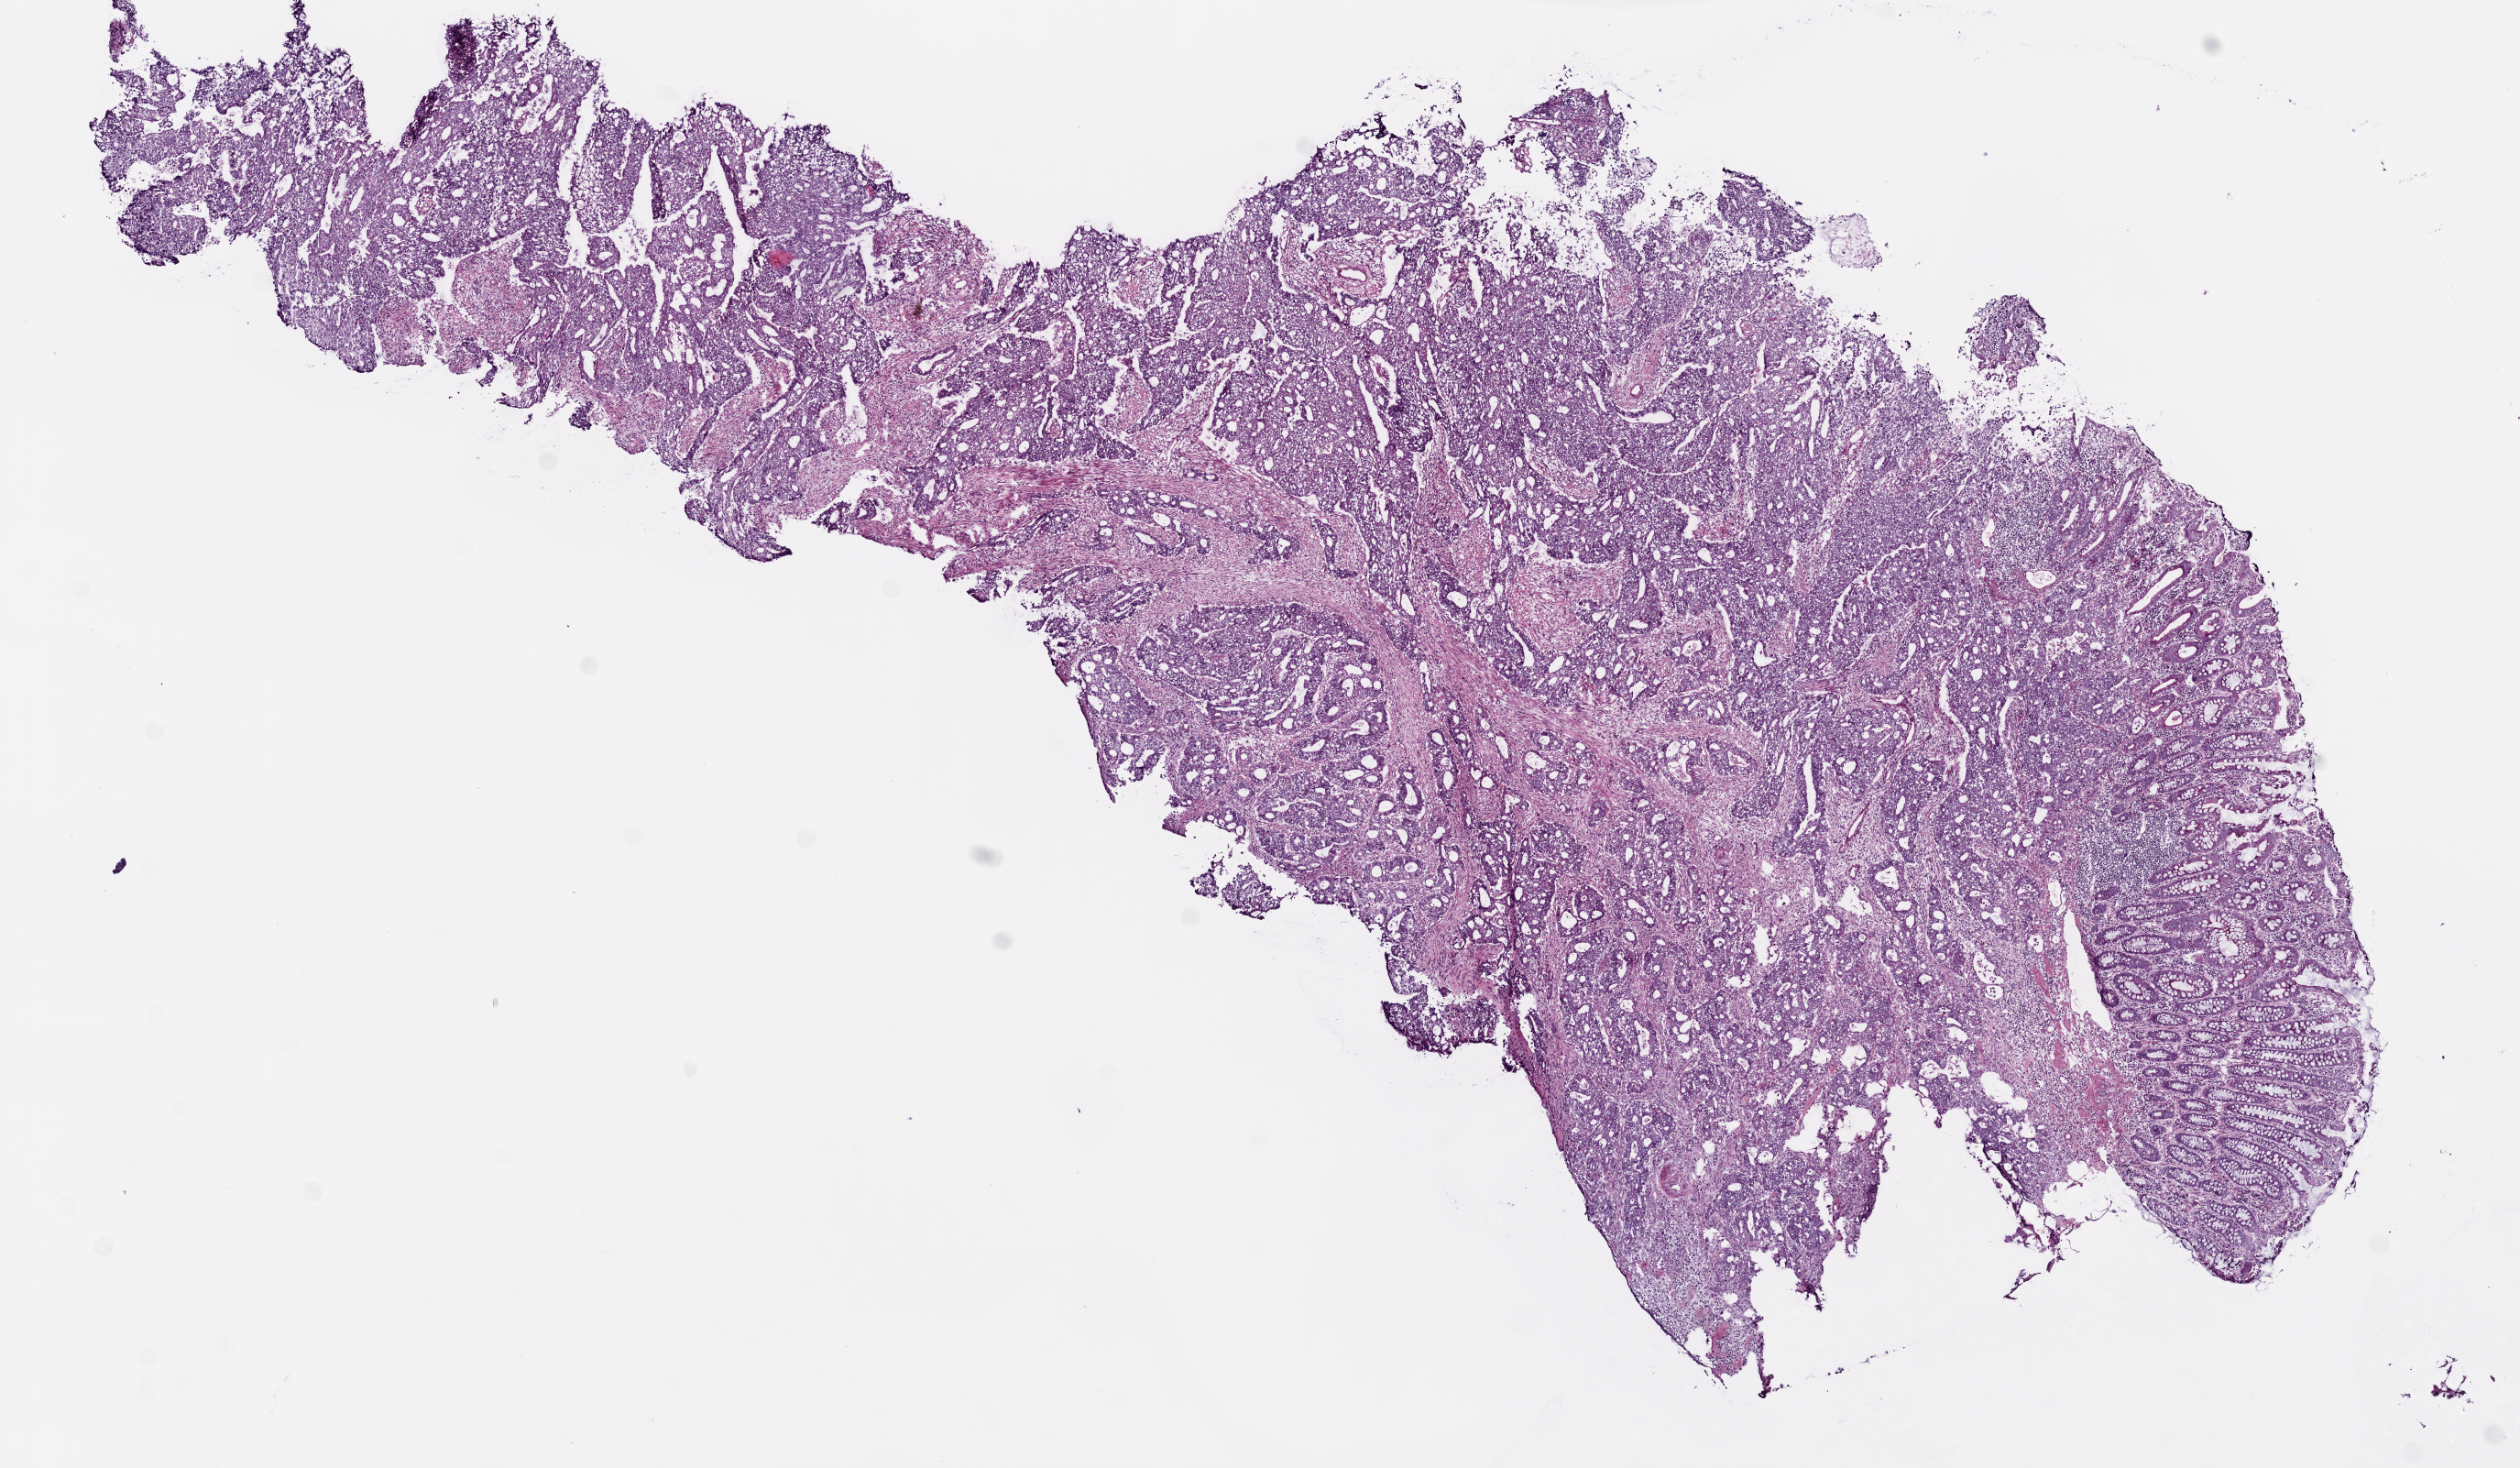
Digitized H&E-stained tissue section (whole slide) — low-resolution overview of the scanned area, about 11.0 x 6.4 mm (slide scanned at 20x), frozen section, sample: primary tumour, colon. Patient: male, age at initial diagnosis 62 years. Pathologist review of this section (percent, as recorded): tumour cells 70%, tumour nuclei 80%, normal cells 10%, stromal cells 15%, necrosis 5%.
• AJCC pathologic stage: IIIB (7th edition)
• lymph nodes positive (case pathology): 3 of 48 examined
• pathologic diagnosis: Adenocarcinoma, NOS (cecum)